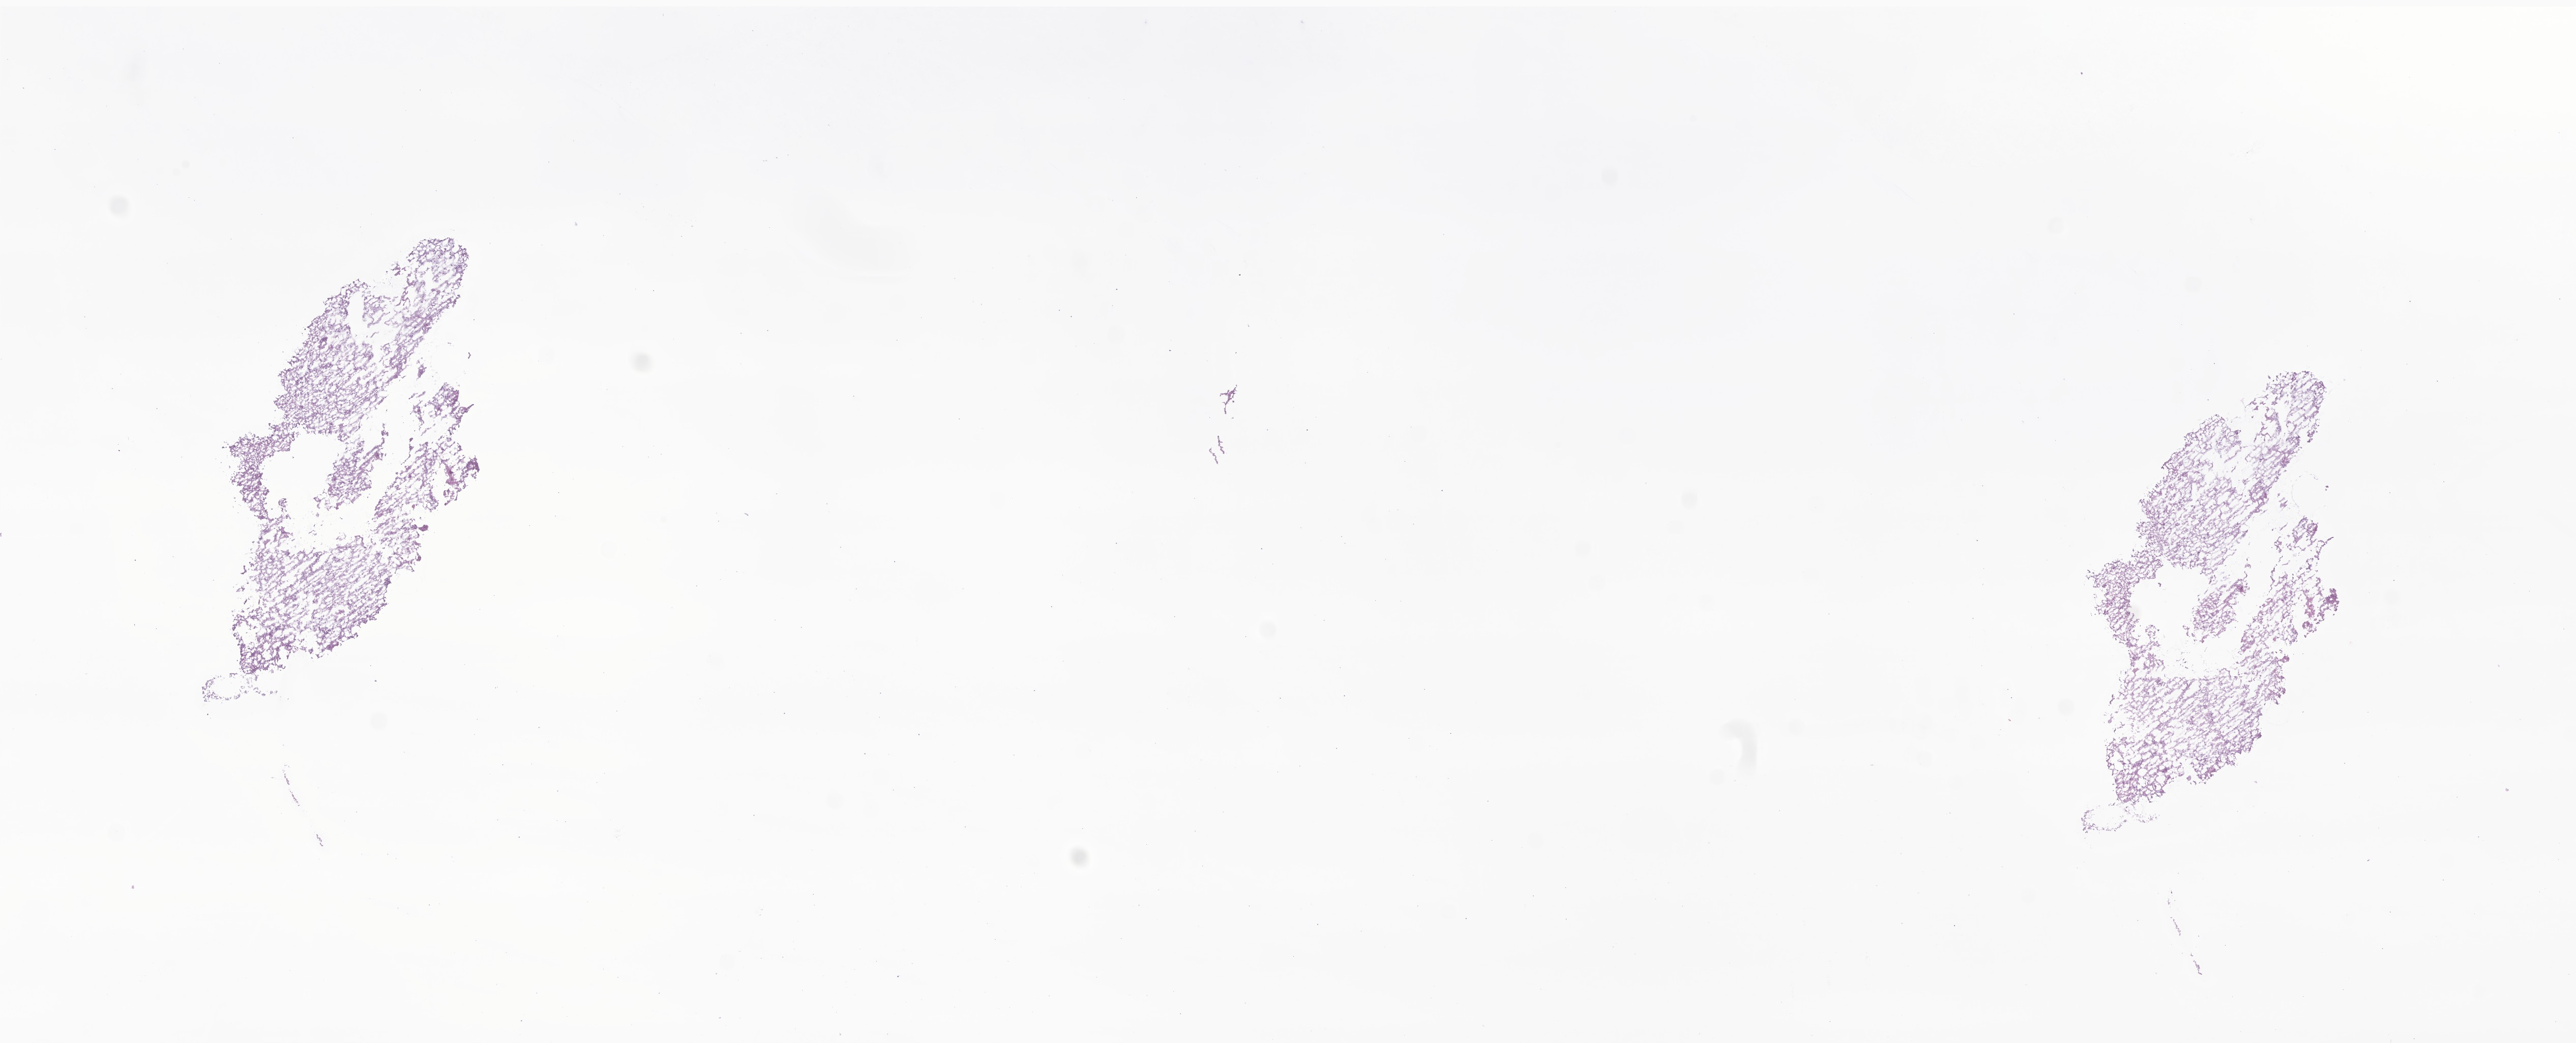
Digitized hematoxylin and eosin (H&E)-stained section of tumor tissue from the brain, shown as a low-resolution overview of the whole scanned area (about 21.4 x 8.6 mm). Frozen section (OCT-embedded). Male patient, age 88 months (7 years 4 months).
Diagnosis (ICD-O-3 morphology term): Neoplasm, malignant.